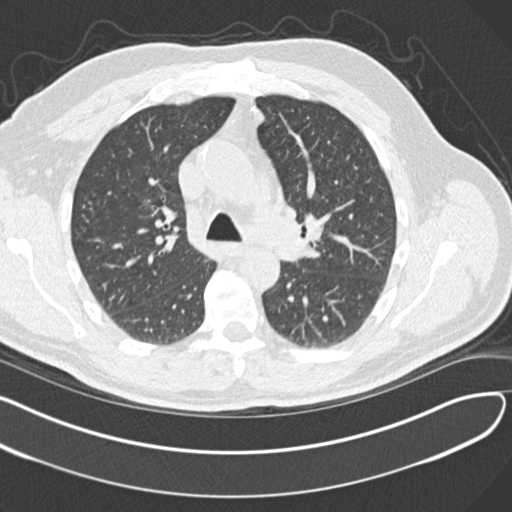
Chest CT (low-dose screening protocol), one axial image; second screening round (one year after baseline); lung window (W 1500 / L -600 HU); standard (soft-tissue) reconstruction kernel (B30f); 512 × 512 image matrix. Male, age 65 years at enrolment. Former smoker at enrolment.
Expert reader's lesion annotation, bounding box [x1, y1, x2, y2] px = [289, 195, 352, 259]. The screening reader recorded 4 non-calcified nodules or masses ≥4 mm on this exam; which of them this box marks is not recorded. Lung cancer was diagnosed 577 days after this screen: acinar cell carcinoma, left upper lobe, stage IA (AJCC 6th edition), 25 mm at pathology.